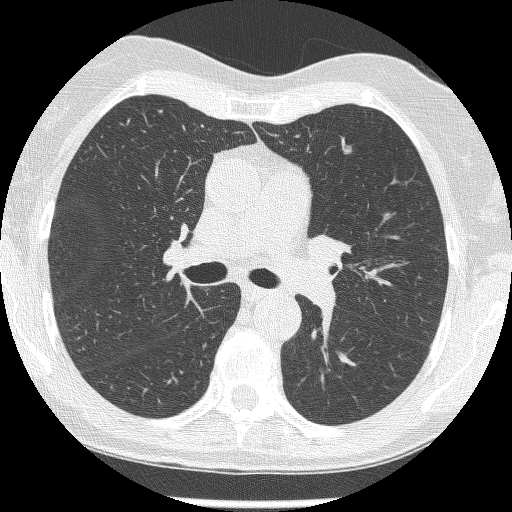
Low-dose screening chest CT, axial slice. Second annual screen. Lung window (W 1500 / L -600 HU). 120 kVp. Female, age 60 years at enrolment.
Expert reader's lesion annotation, bounding box (x1, y1, x2, y2) in pixels: (331, 138, 361, 162). The screening reader recorded 2 non-calcified nodules or masses ≥4 mm on this exam (left upper lobe, left upper lobe); which of them this box marks is not recorded. Official screen result: positive, change unspecified: nodule(s) >= 4 mm or enlarging nodule(s), mass(es), or other non-specific abnormalities suspicious for lung cancer.